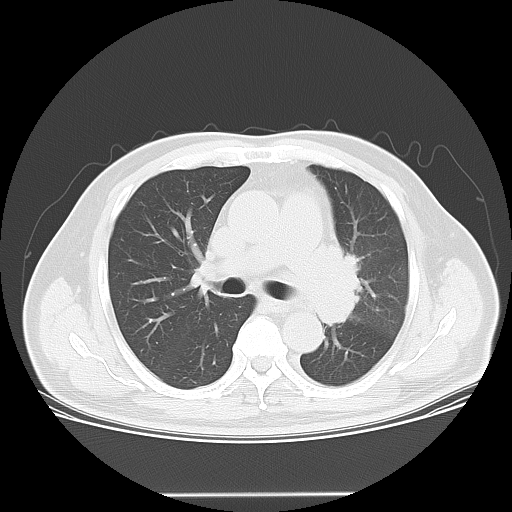
Chest CT, one axial slice; position 35 of 55 along the scan axis; 120 kVp; lung window (W 1500 / L -600 HU); 512 × 512 image matrix. Male patient, age 61 years. Case-level facts recorded for this patient, not image findings: clinical TNM (as recorded): T3 N1 M1; histopathological grade: G3.
Structures marked on this image (rectangle marked by the reading radiologist):
- lung tumour (recorded histology: small cell carcinoma): bounding box <310,236,374,336> (left, top, right, bottom; pixels)